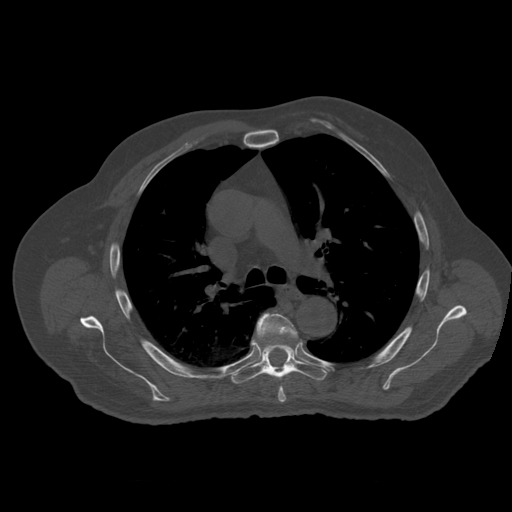
CT including the spine, one axial slice. Position 389 of 399 along the scan axis. Reconstruction kernel STANDARD. 120 kVp. Bone window (W 1800 / L 400 HU). 1.25 mm slice thickness. 512 × 512 image matrix. Patient age 73 years. Case-level facts recorded for this patient, not image findings: primary cancer: prostate; vertebrae with lytic lesions (as recorded): L2.
Structures marked on this image (semi-automatically segmented with operator editing):
- T5 vertebra: bounding box <257,313,298,403> (left, top, right, bottom; pixels)
- T6 vertebra: <232,340,327,384>